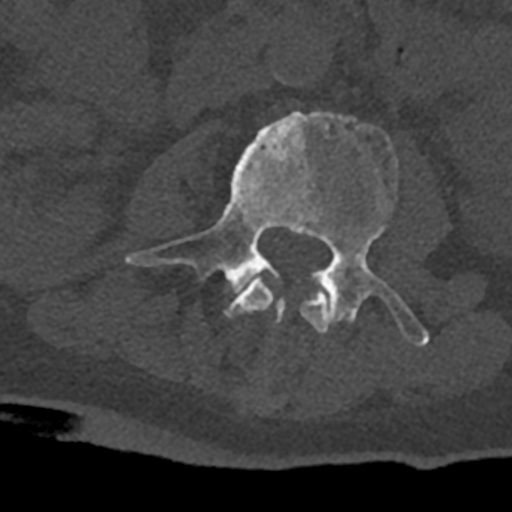
CT including the spine, one axial slice. Position 332 of 797 along the scan axis. Reconstruction kernel Br40s/3. Bone window (W 1800 / L 400 HU). 0.5 mm slice thickness. 512 × 512 image matrix, field of view 160 × 160 mm. Male patient, age 74 years. Case-level facts recorded for this patient, not image findings: primary cancer: renal; vertebrae with lytic lesions (as recorded): T10, L1, L2, L3, L4, L5.
Annotated regions visible in this slice (semi-automatically segmented with operator editing):
- L2 vertebra: box from (x=226, y=278) to (x=329, y=333) px
- L3 vertebra: (x=125, y=111)–(x=429, y=347)